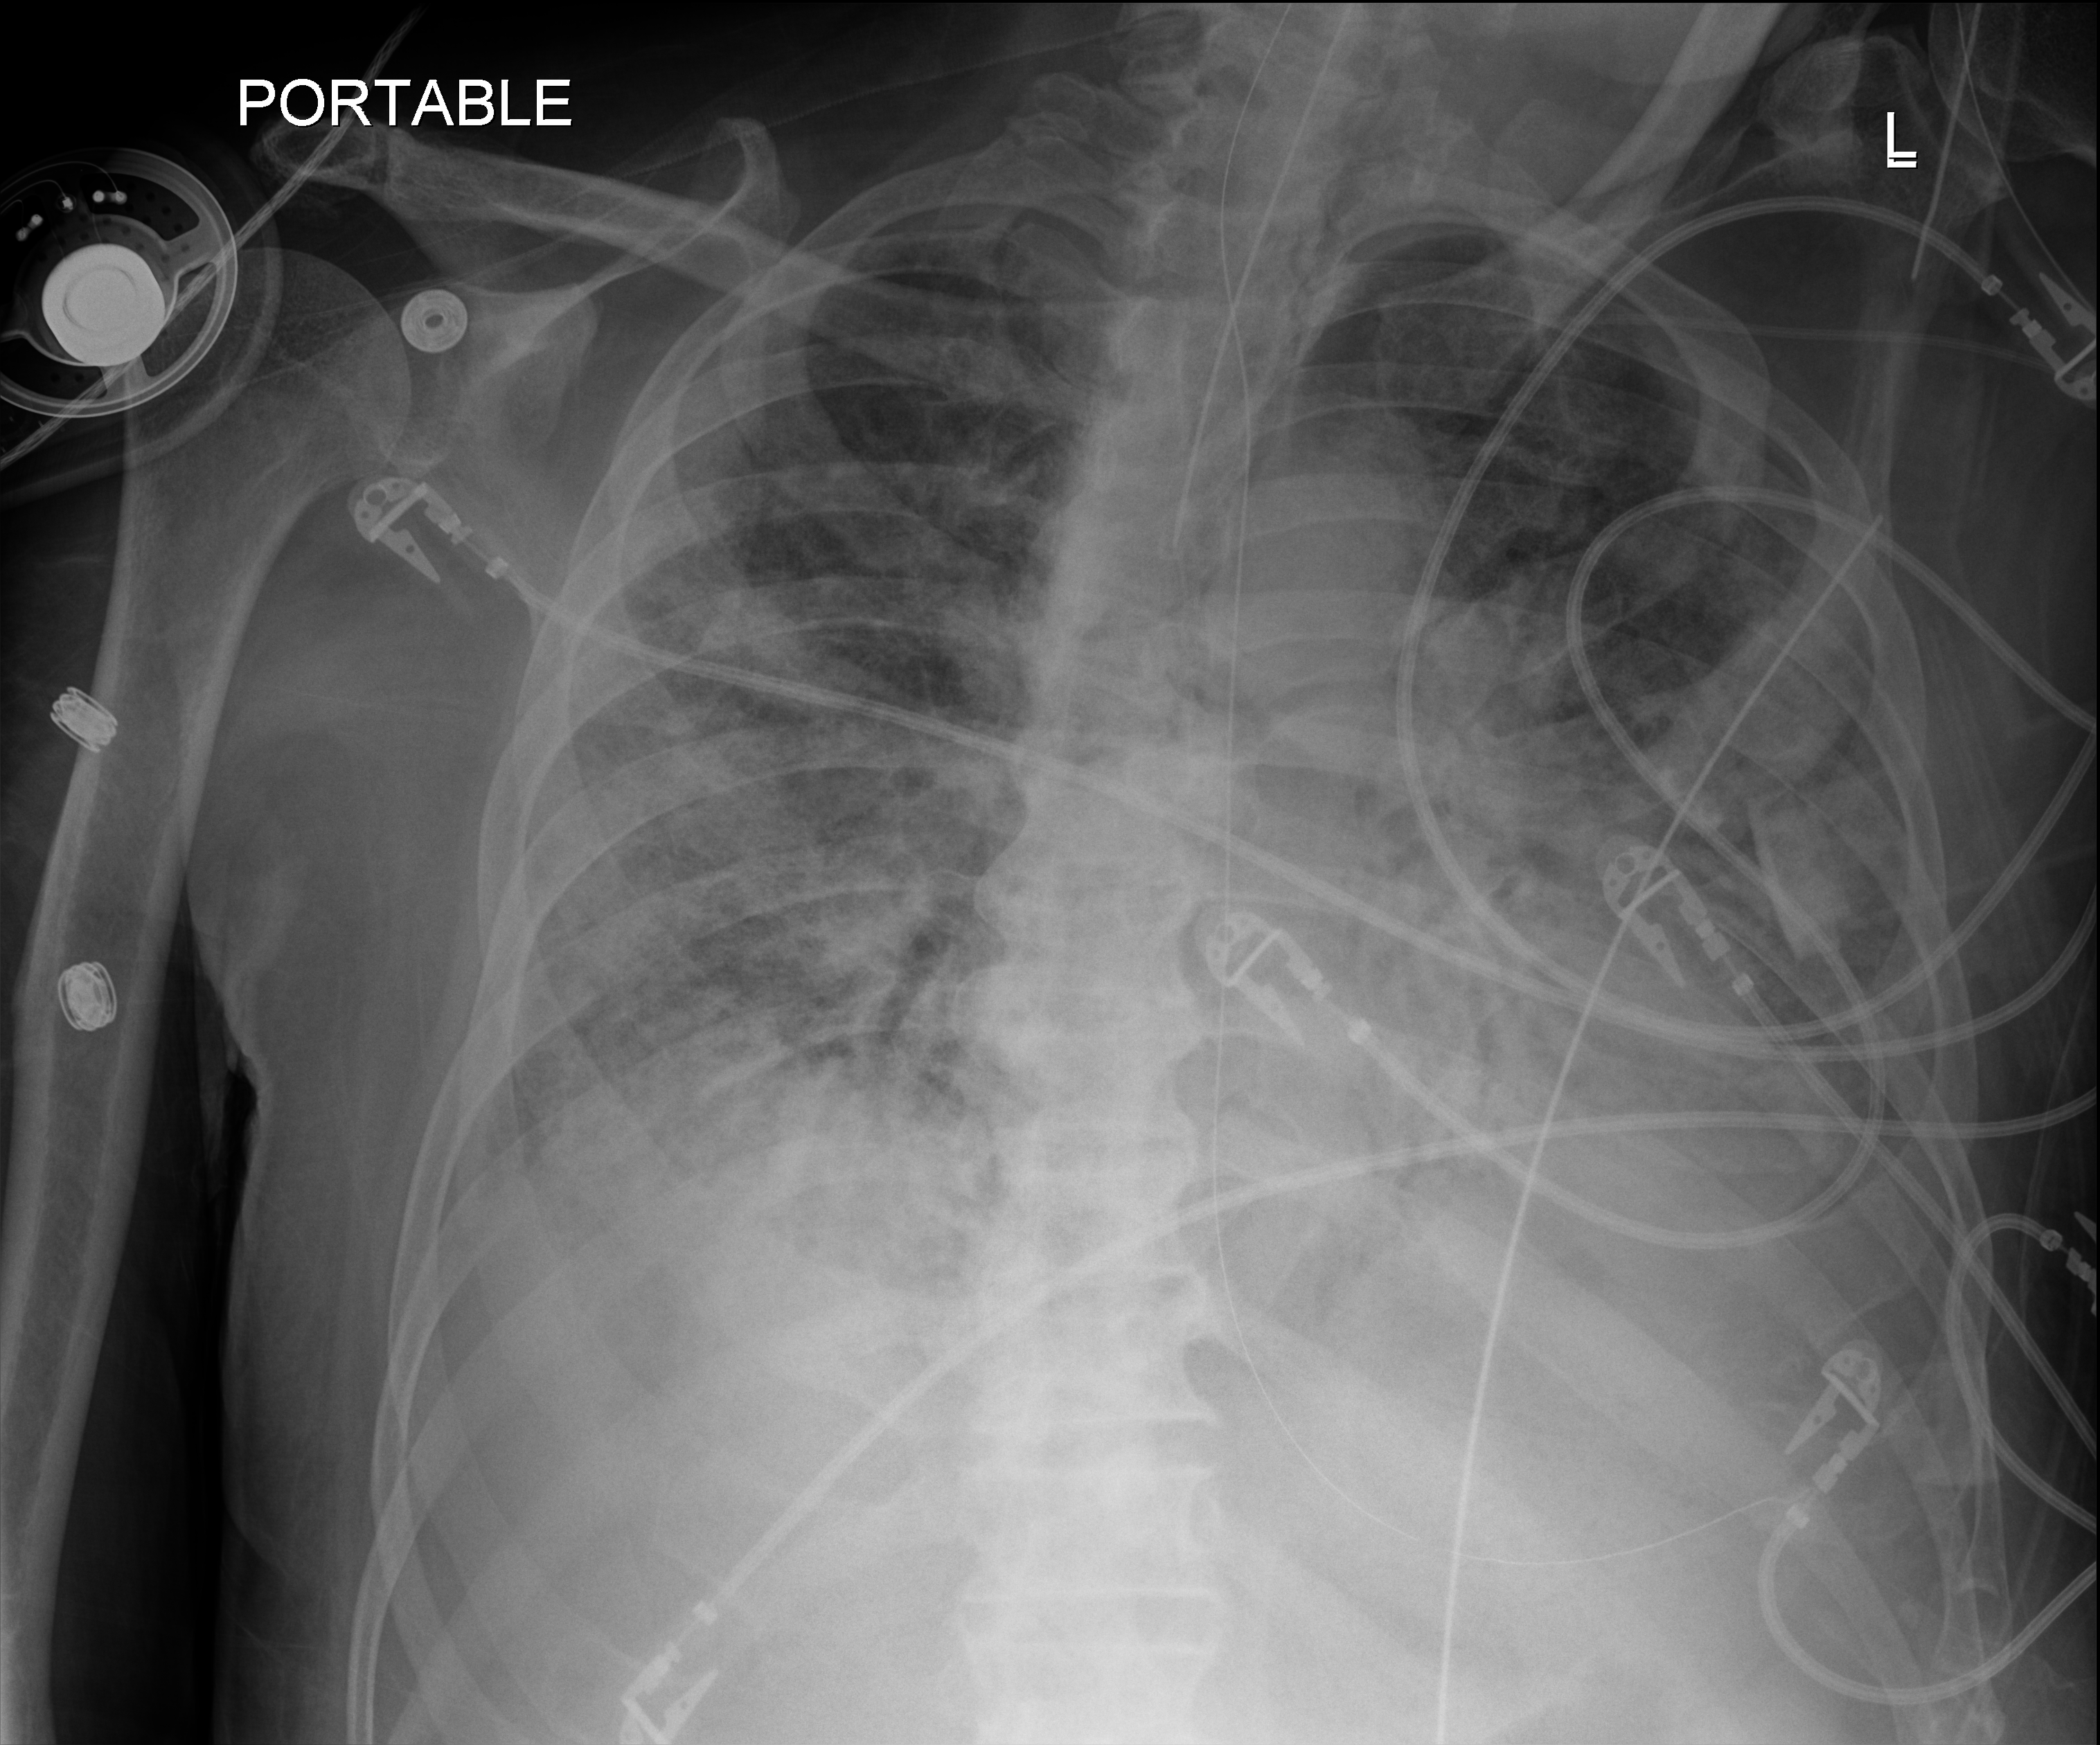
Chest X-ray (portable); anteroposterior (AP) projection. Patient hospitalised with COVID-19; male, aged 75–90 years.
From the hospital-stay record, not from the radiograph (when in the stay this image was taken is not recorded): length of hospital stay: 33 days; mechanically ventilated during this hospital stay: yes.